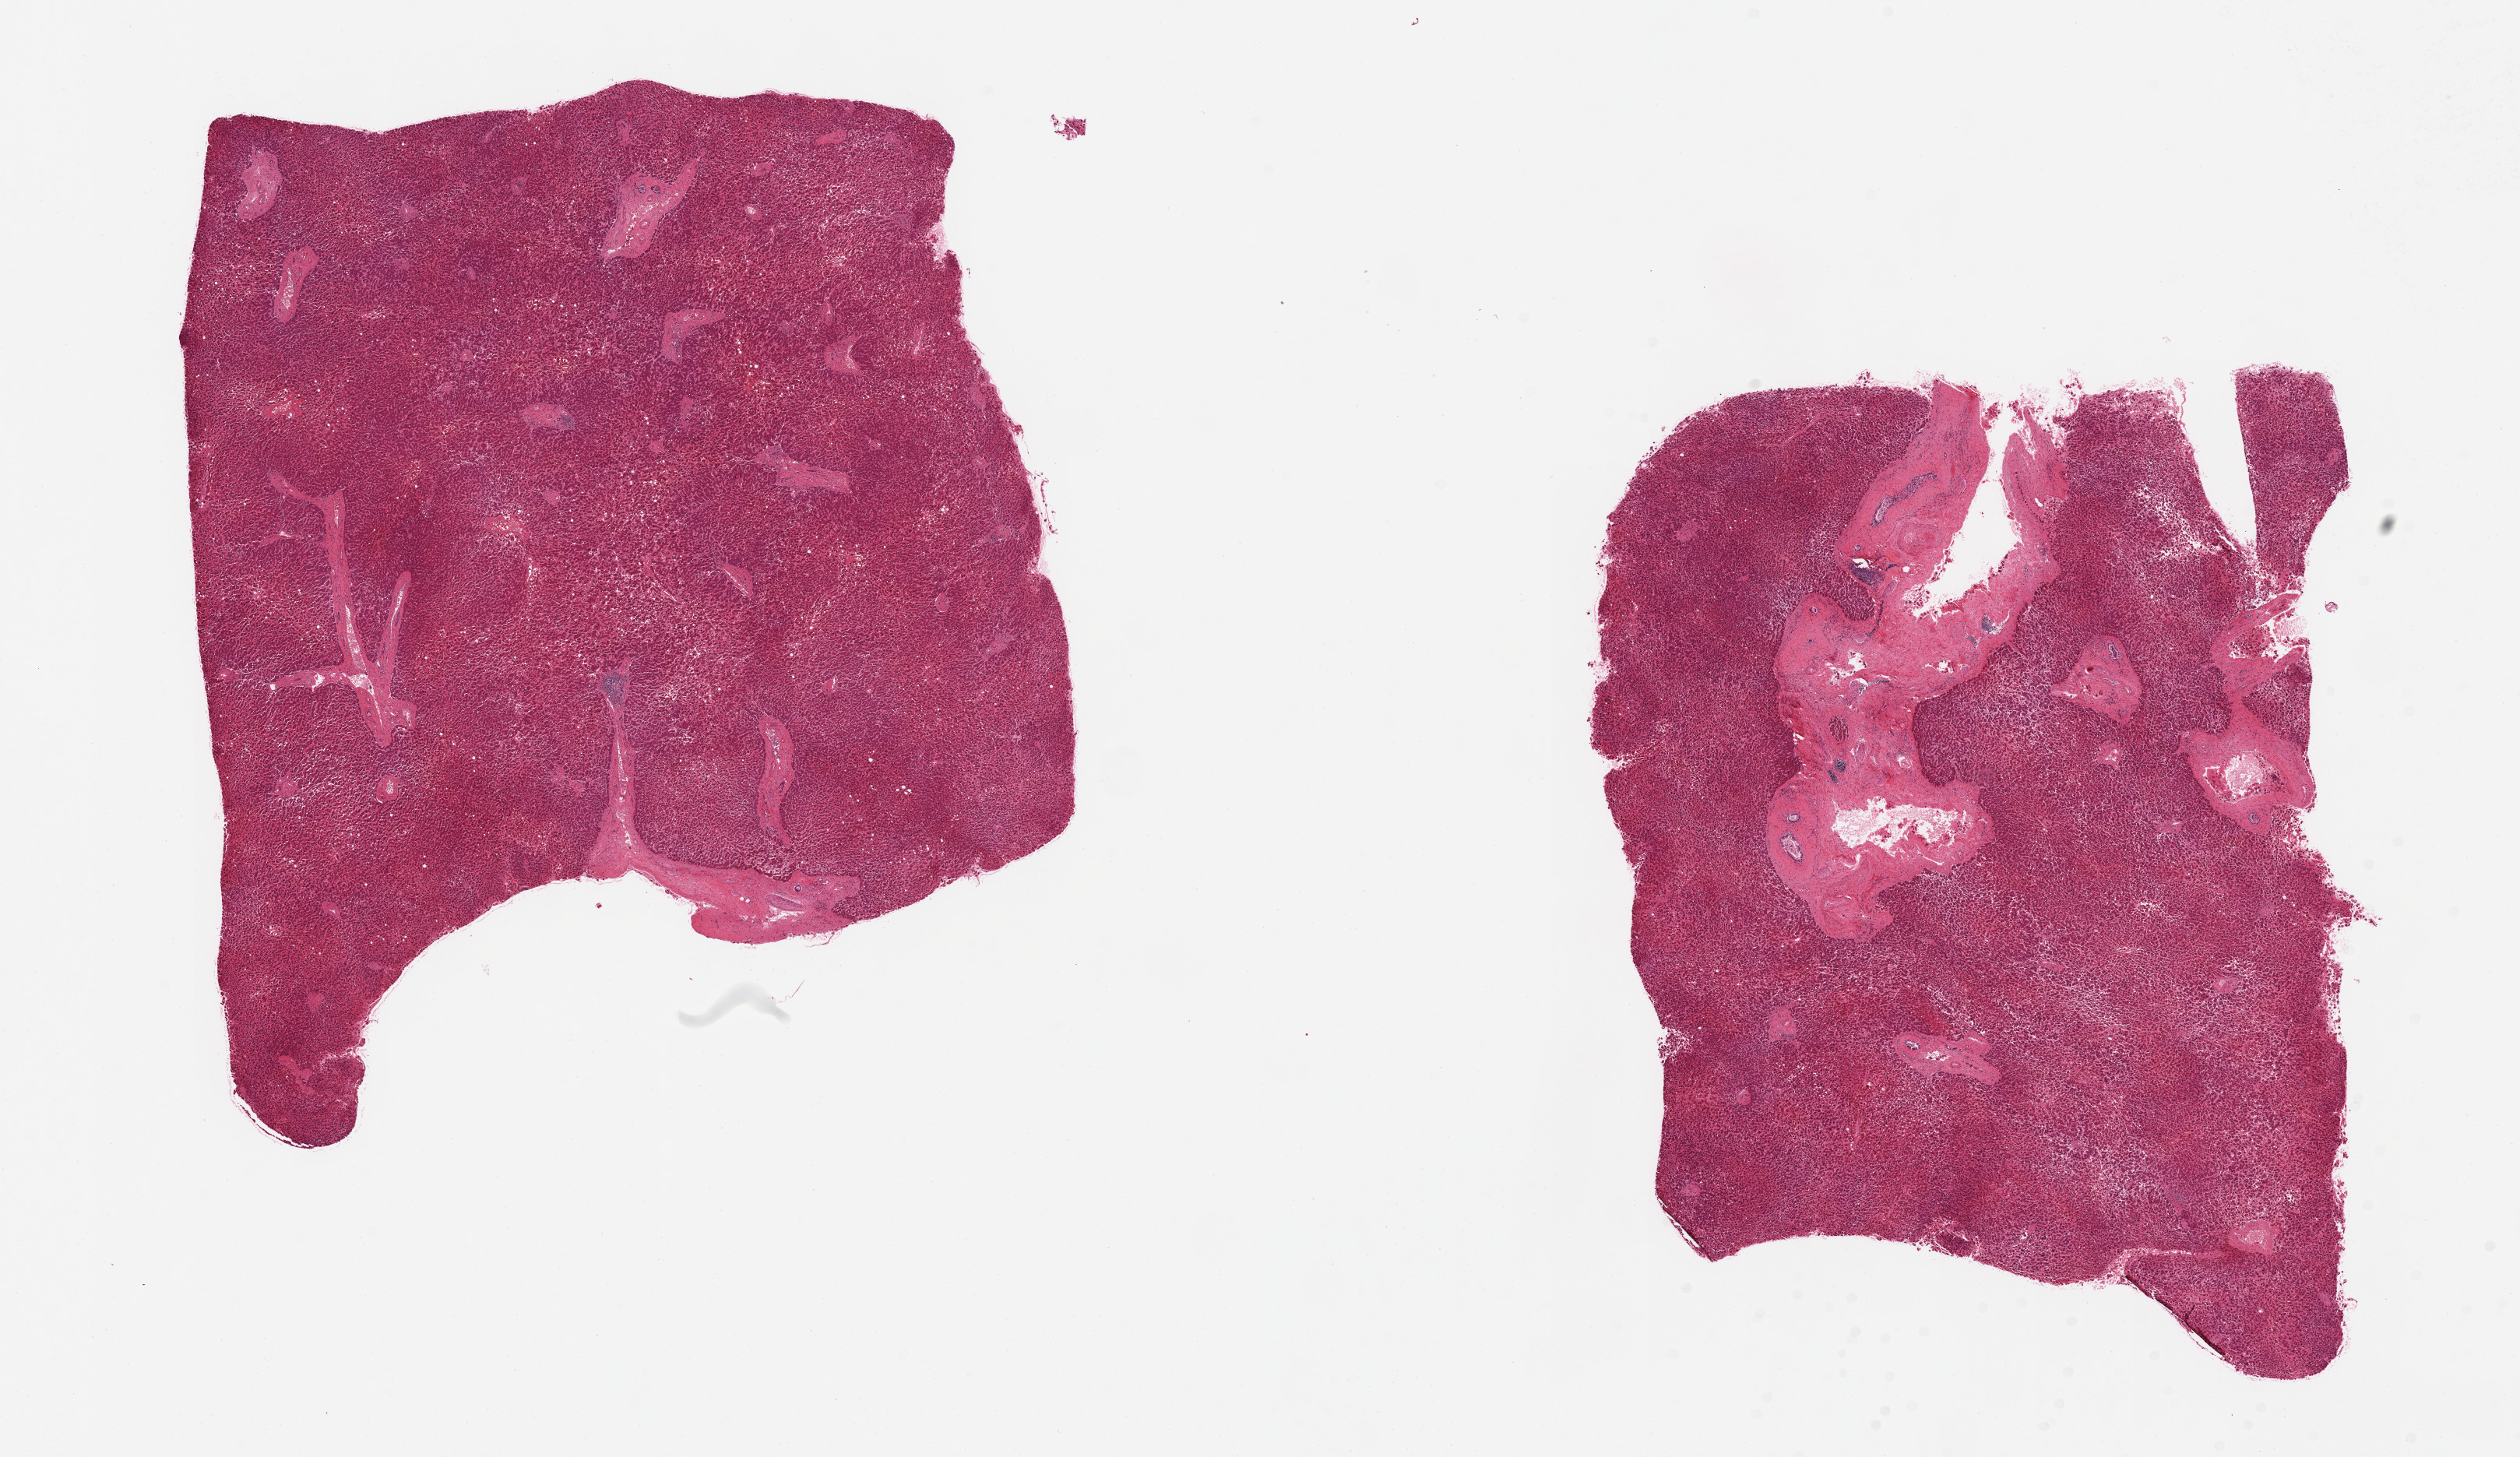
Digitized hematoxylin and eosin (H&E)-stained section — a low-resolution overview of the entire scanned area, about 25.6 x 14.8 mm (slide scanned at 20x), PAXgene-fixed paraffin-embedded (PFPE) section, sampled site (target tissue): liver, tissue donor sample. Donor sex: male.
Reviewer comment on this tissue sample: 2 pieces, mild steatosis.